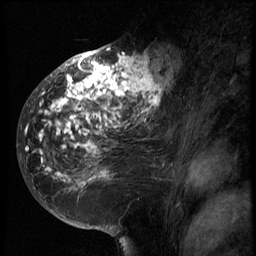
Breast MRI (dynamic contrast-enhanced), one sagittal slice; slice 36 of 66 in the series (ordered by position); 3 images stored at this slice position (order not interpretable as contrast timing); 1.5 T; TE 4.2 ms, TR 8.9 ms; 2.5 mm slice thickness; 256 × 256 image matrix, field of view 200 × 200 mm. Patient: female, 39 years. From the clinical record (not read from this slice): setting: breast cancer imaged before/during neoadjuvant chemotherapy; receptor status: HER2-positive.
Outlined on this slice (semi-automatically segmented with operator editing):
- analysis volume of interest (the breast-tissue region the enhancement analysis was run in; not a lesion): box from (x=29, y=44) to (x=166, y=196) px
- tumour enhancement mask (voxels above the 140 % enhancement threshold inside the analysis volume of interest): (x=34, y=47)–(x=166, y=179)